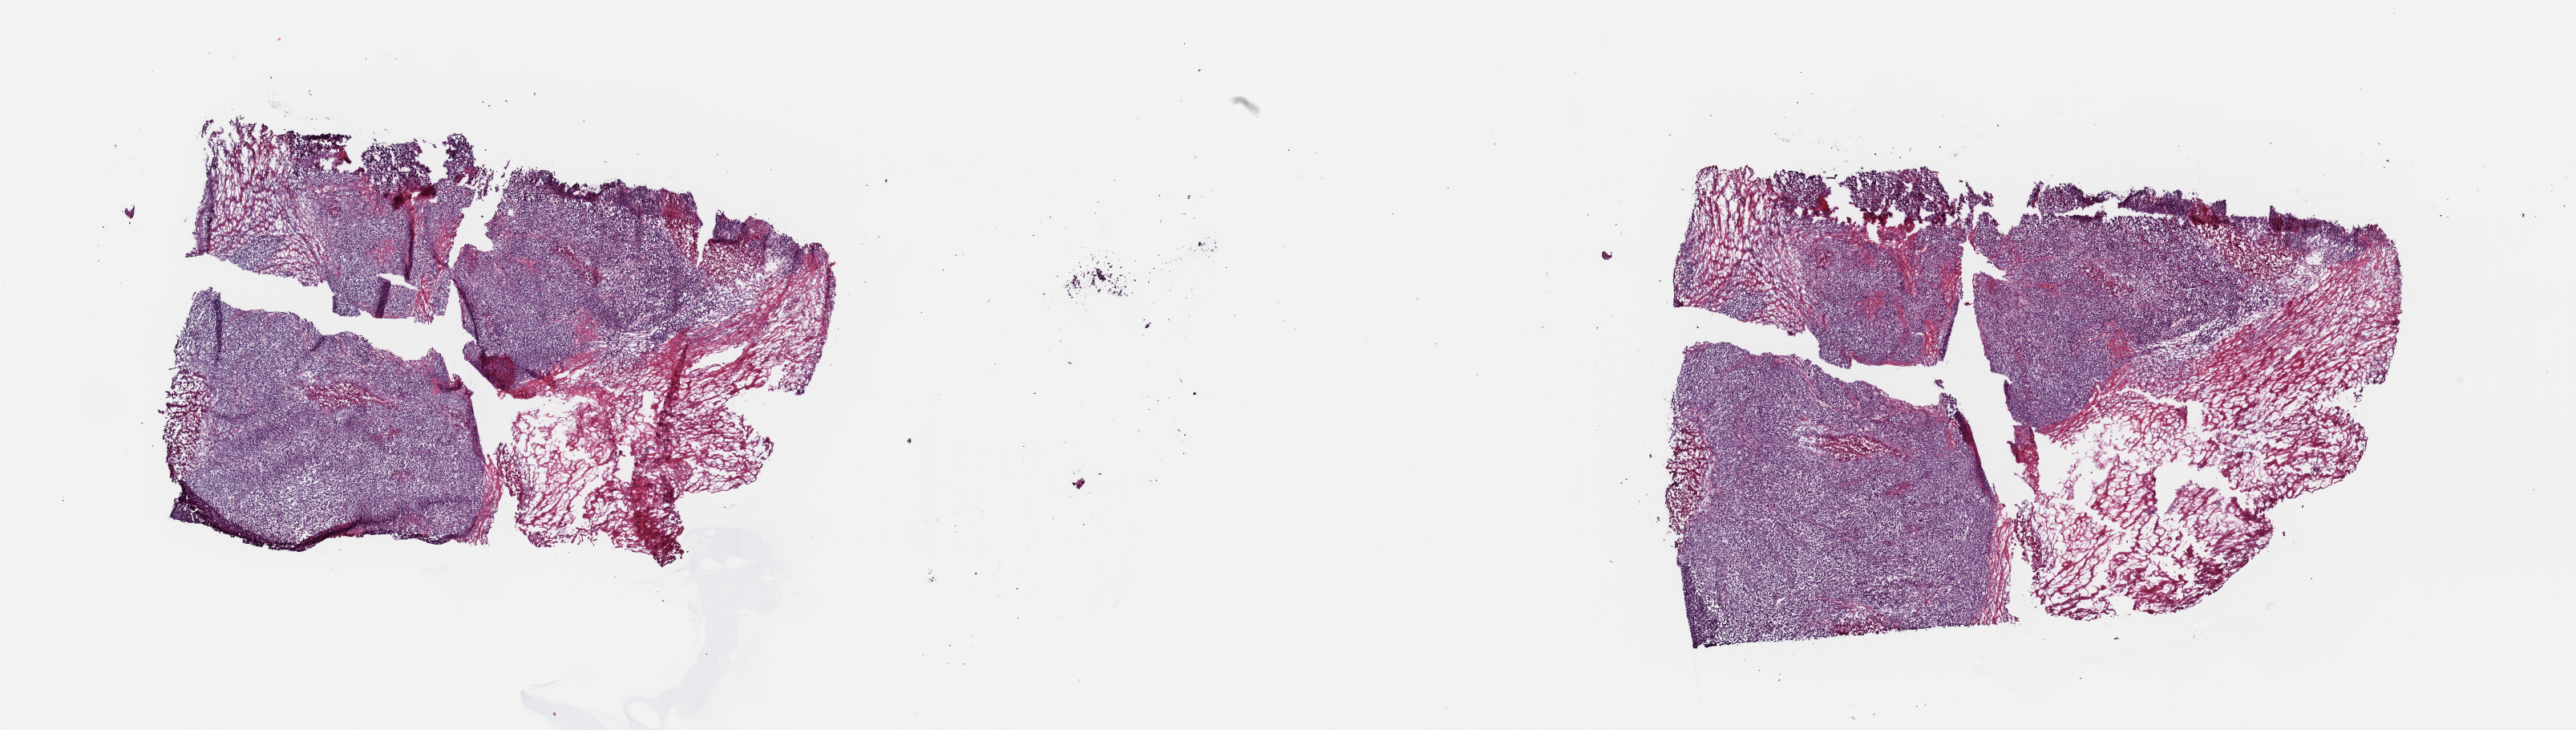
Whole-slide histology image, H&E-stained — whole scanned area (about 25.4 x 7.2 mm, from a 40x scan) shown as a low-resolution overview. Frozen section. Metastatic tumour sample. Patient: male, age at initial diagnosis 36 years. Pathologist review of this section (percent, as recorded): tumour cells 65%, tumour nuclei 85%, normal cells 0%, stromal cells 25%, necrosis 10%. Infiltration values recorded for this section: lymphocyte infiltration 0%, monocyte infiltration 0%, neutrophil infiltration 0%.
This section: metastatic tumour tissue. Patient diagnosis: Malignant melanoma, NOS.